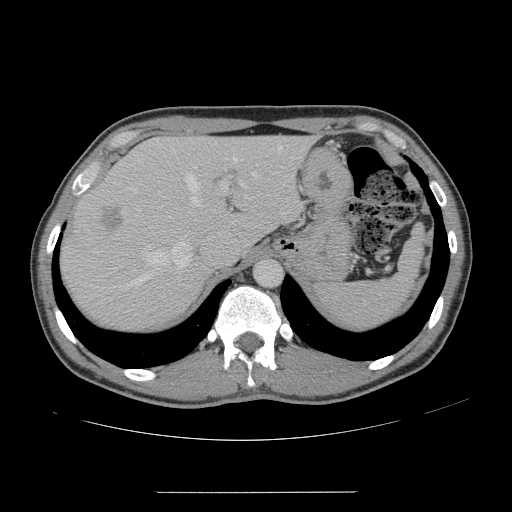
Contrast-enhanced abdominal CT, one axial slice; slice 114 of 178 in the series (ordered by position); 120 kVp; intravenous contrast given; soft-tissue window (W 400 / L 40 HU); 2.5 mm slice thickness; 512 × 512 image matrix, field of view 401 × 401 mm. Male patient, age 53 years. Case-level facts recorded for this patient, not image findings: diagnosis: colorectal cancer liver metastases, imaged before liver resection; multiple liver metastases: yes; largest metastasis: 2.4 cm; disease in both lobes: no.
Annotated regions visible in this slice (manually delineated by an expert):
- hepatic veins: bounding box <129,146,281,285> (left, top, right, bottom; pixels)
- liver: <63,137,309,329>
- planned liver remnant (the part of the liver to remain after resection): <147,136,310,247>
- portal vein (with intrahepatic branches): <139,182,247,211>
- liver metastasis: <102,207,124,231>